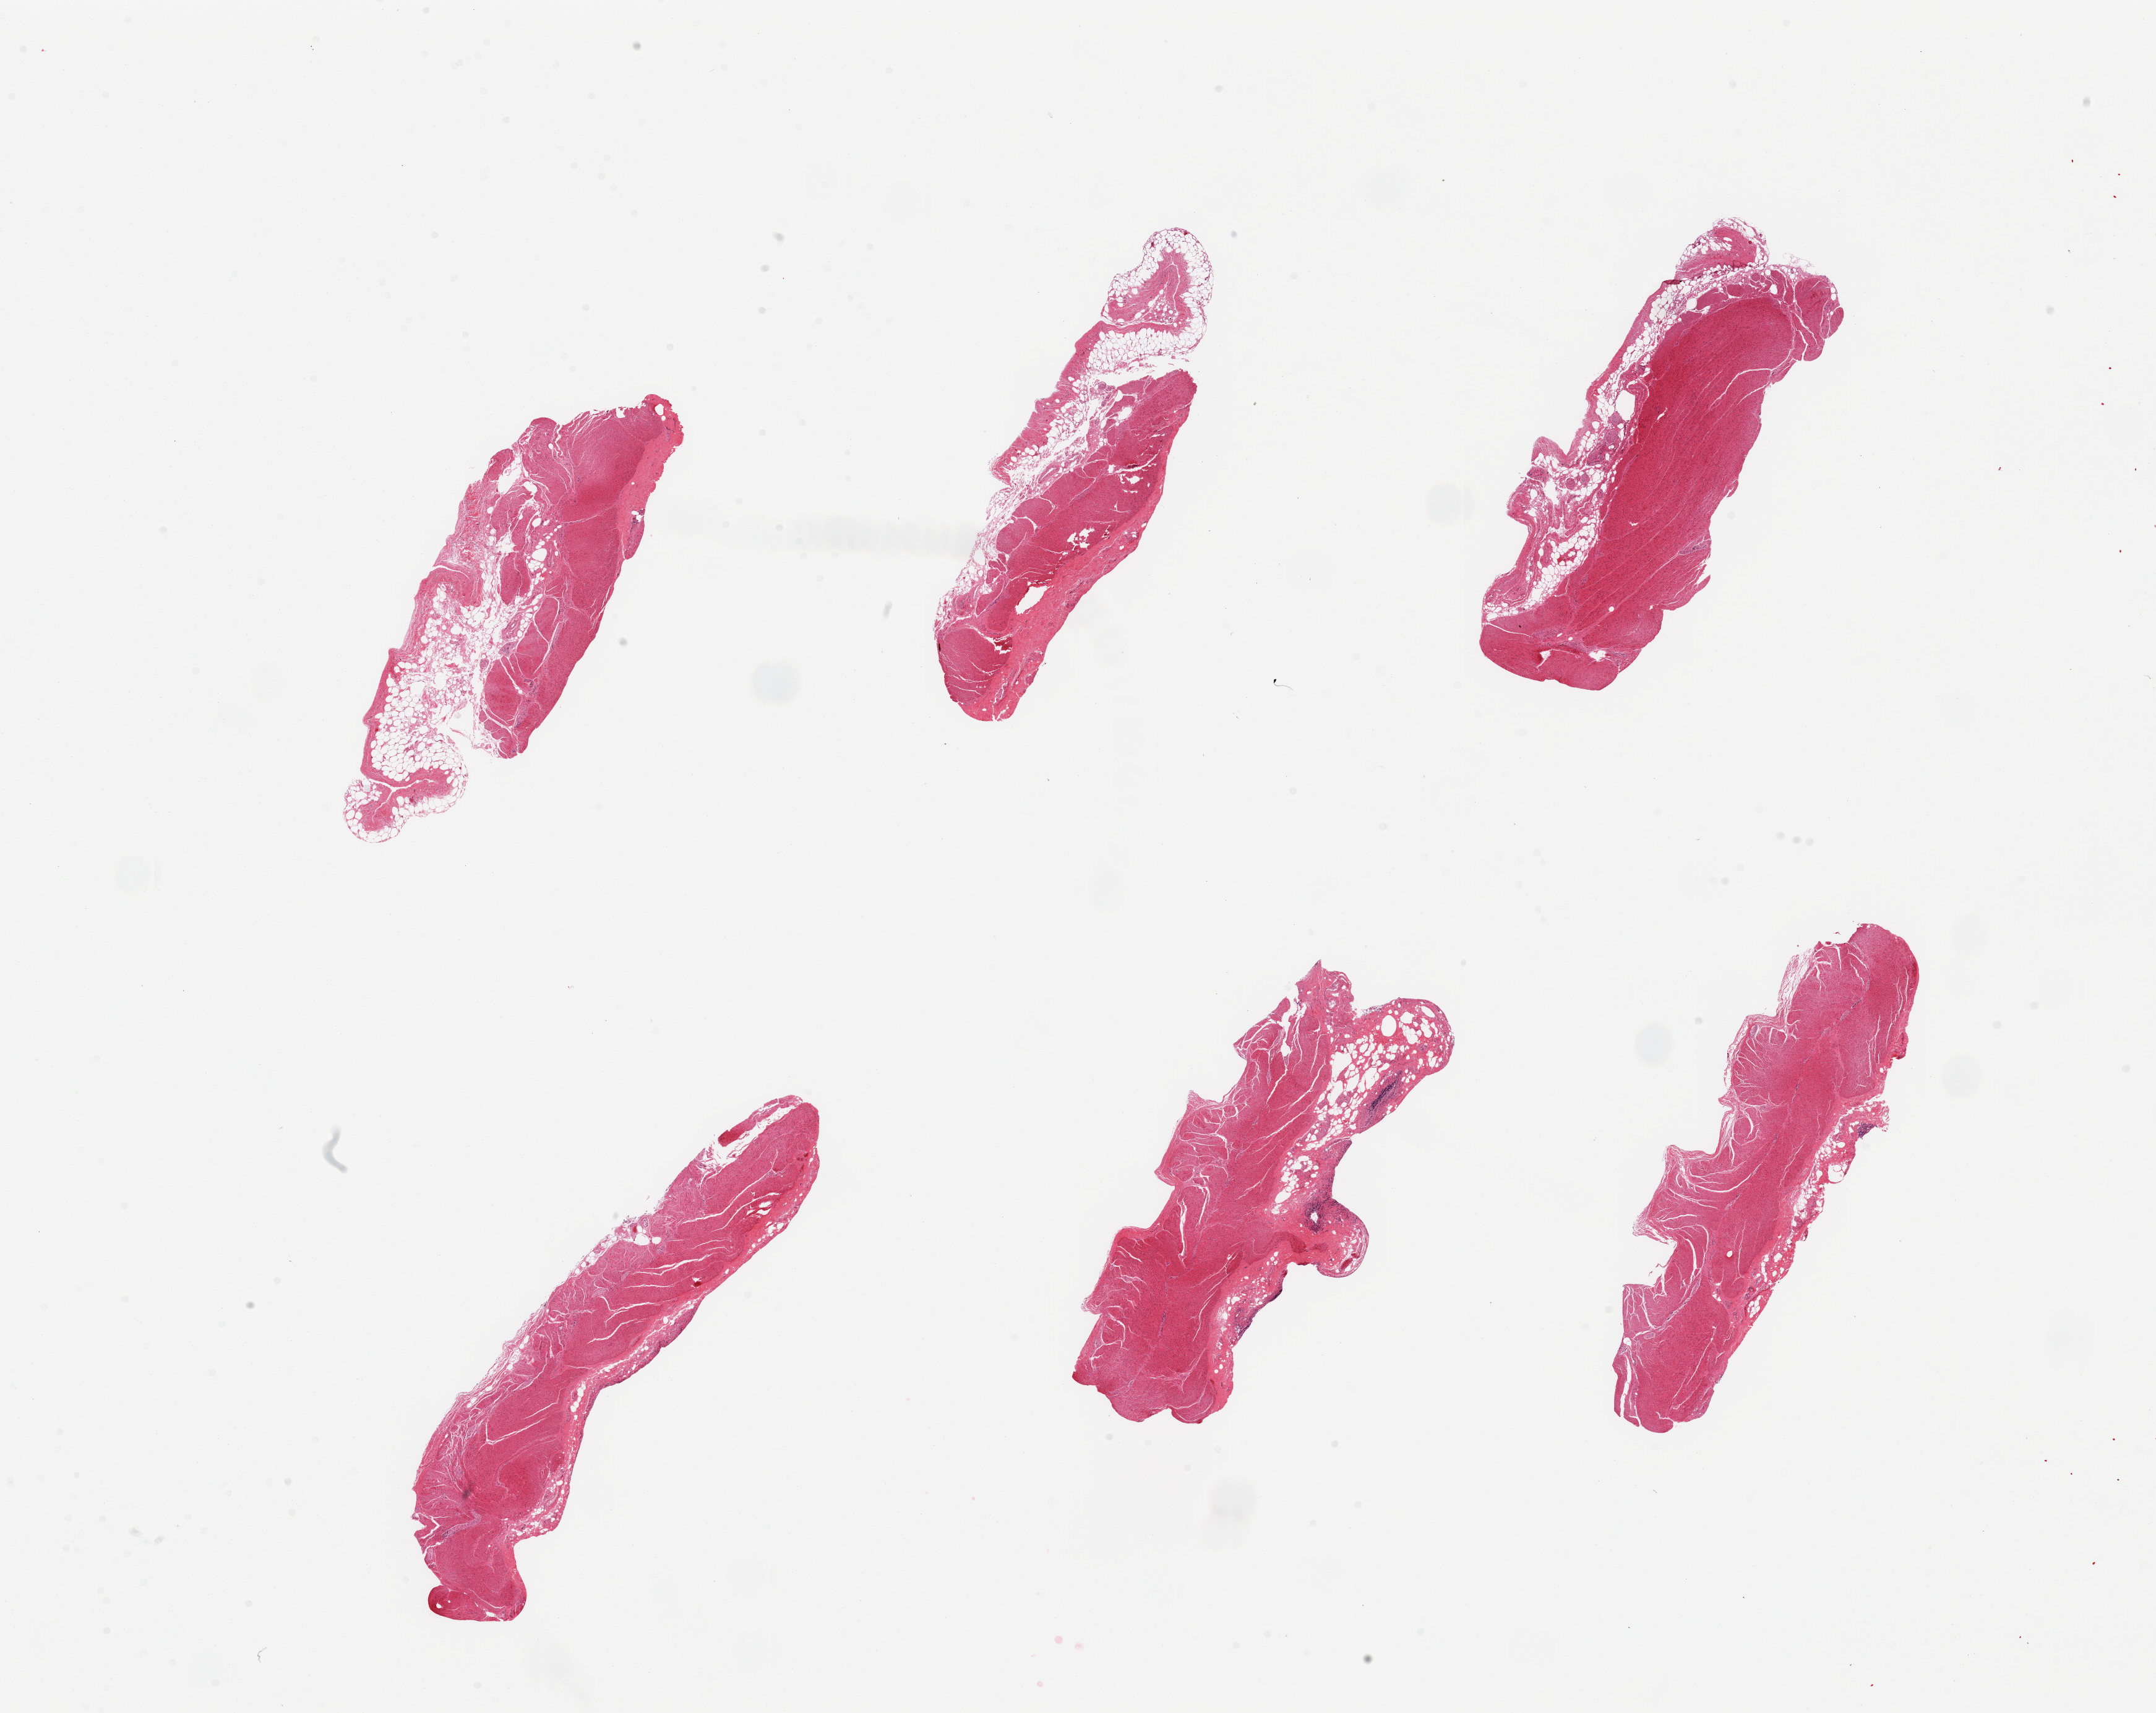
Hematoxylin and eosin (H&E) whole-slide image, whole scanned area (about 27.6 x 21.9 mm, acquisition: 20x scan) shown as a low-resolution overview; PAXgene-fixed paraffin-embedded (PFPE) section; sampled site (target tissue): sigmoid colon; donor tissue sample. Donor sex: male.
Review note (as recorded): 6 pieces; mostly muscularis, but several include significant component of residual fat/submucosa/autolyzed mucosa.